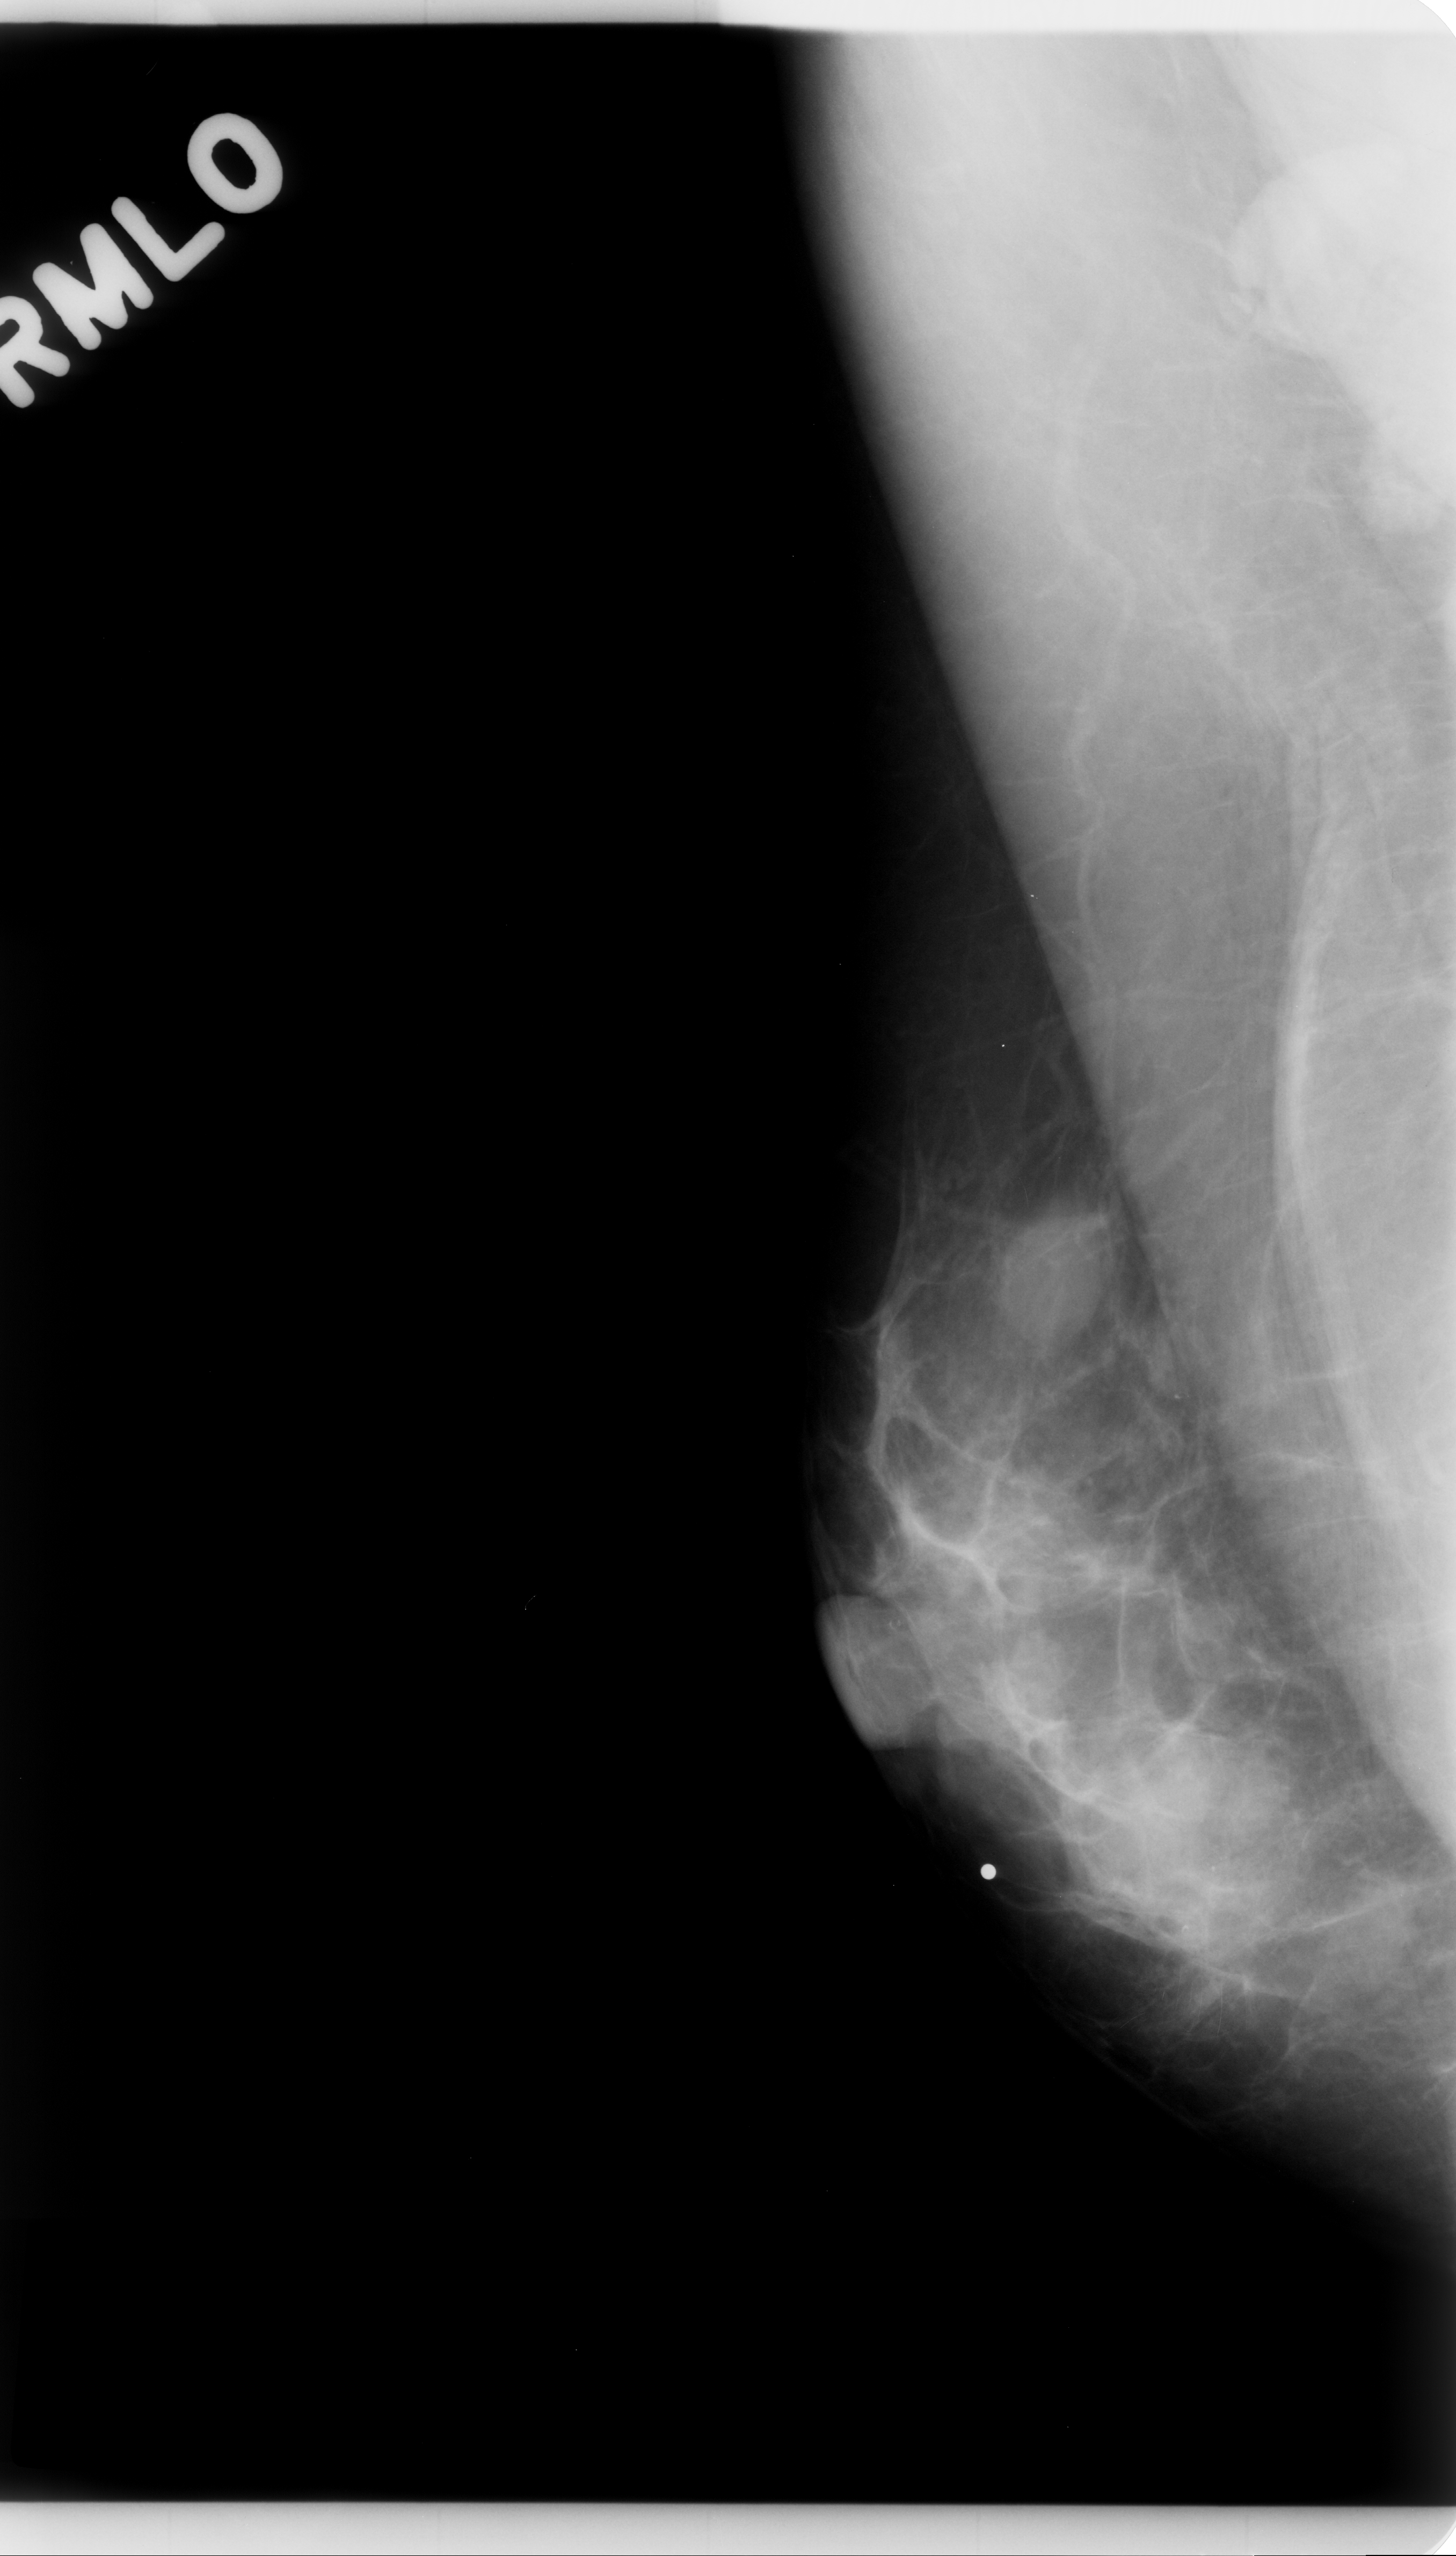
Mammogram (digitized film). Right breast. MLO view. Breast composition: scattered fibroglandular densities (BI-RADS density category 2 of 4). 1456 × 2556 image matrix.
Marked abnormalities (boxes around the expert regions of interest):
- mass, shape oval, margins circumscribed; BI-RADS assessment category 3; subtlety rating 5 on a 1 (subtle) to 5 (obvious) scale; pathology result (as recorded, not read from the image): benign: bounding box [x1, y1, x2, y2] px = [987, 1199, 1115, 1348]